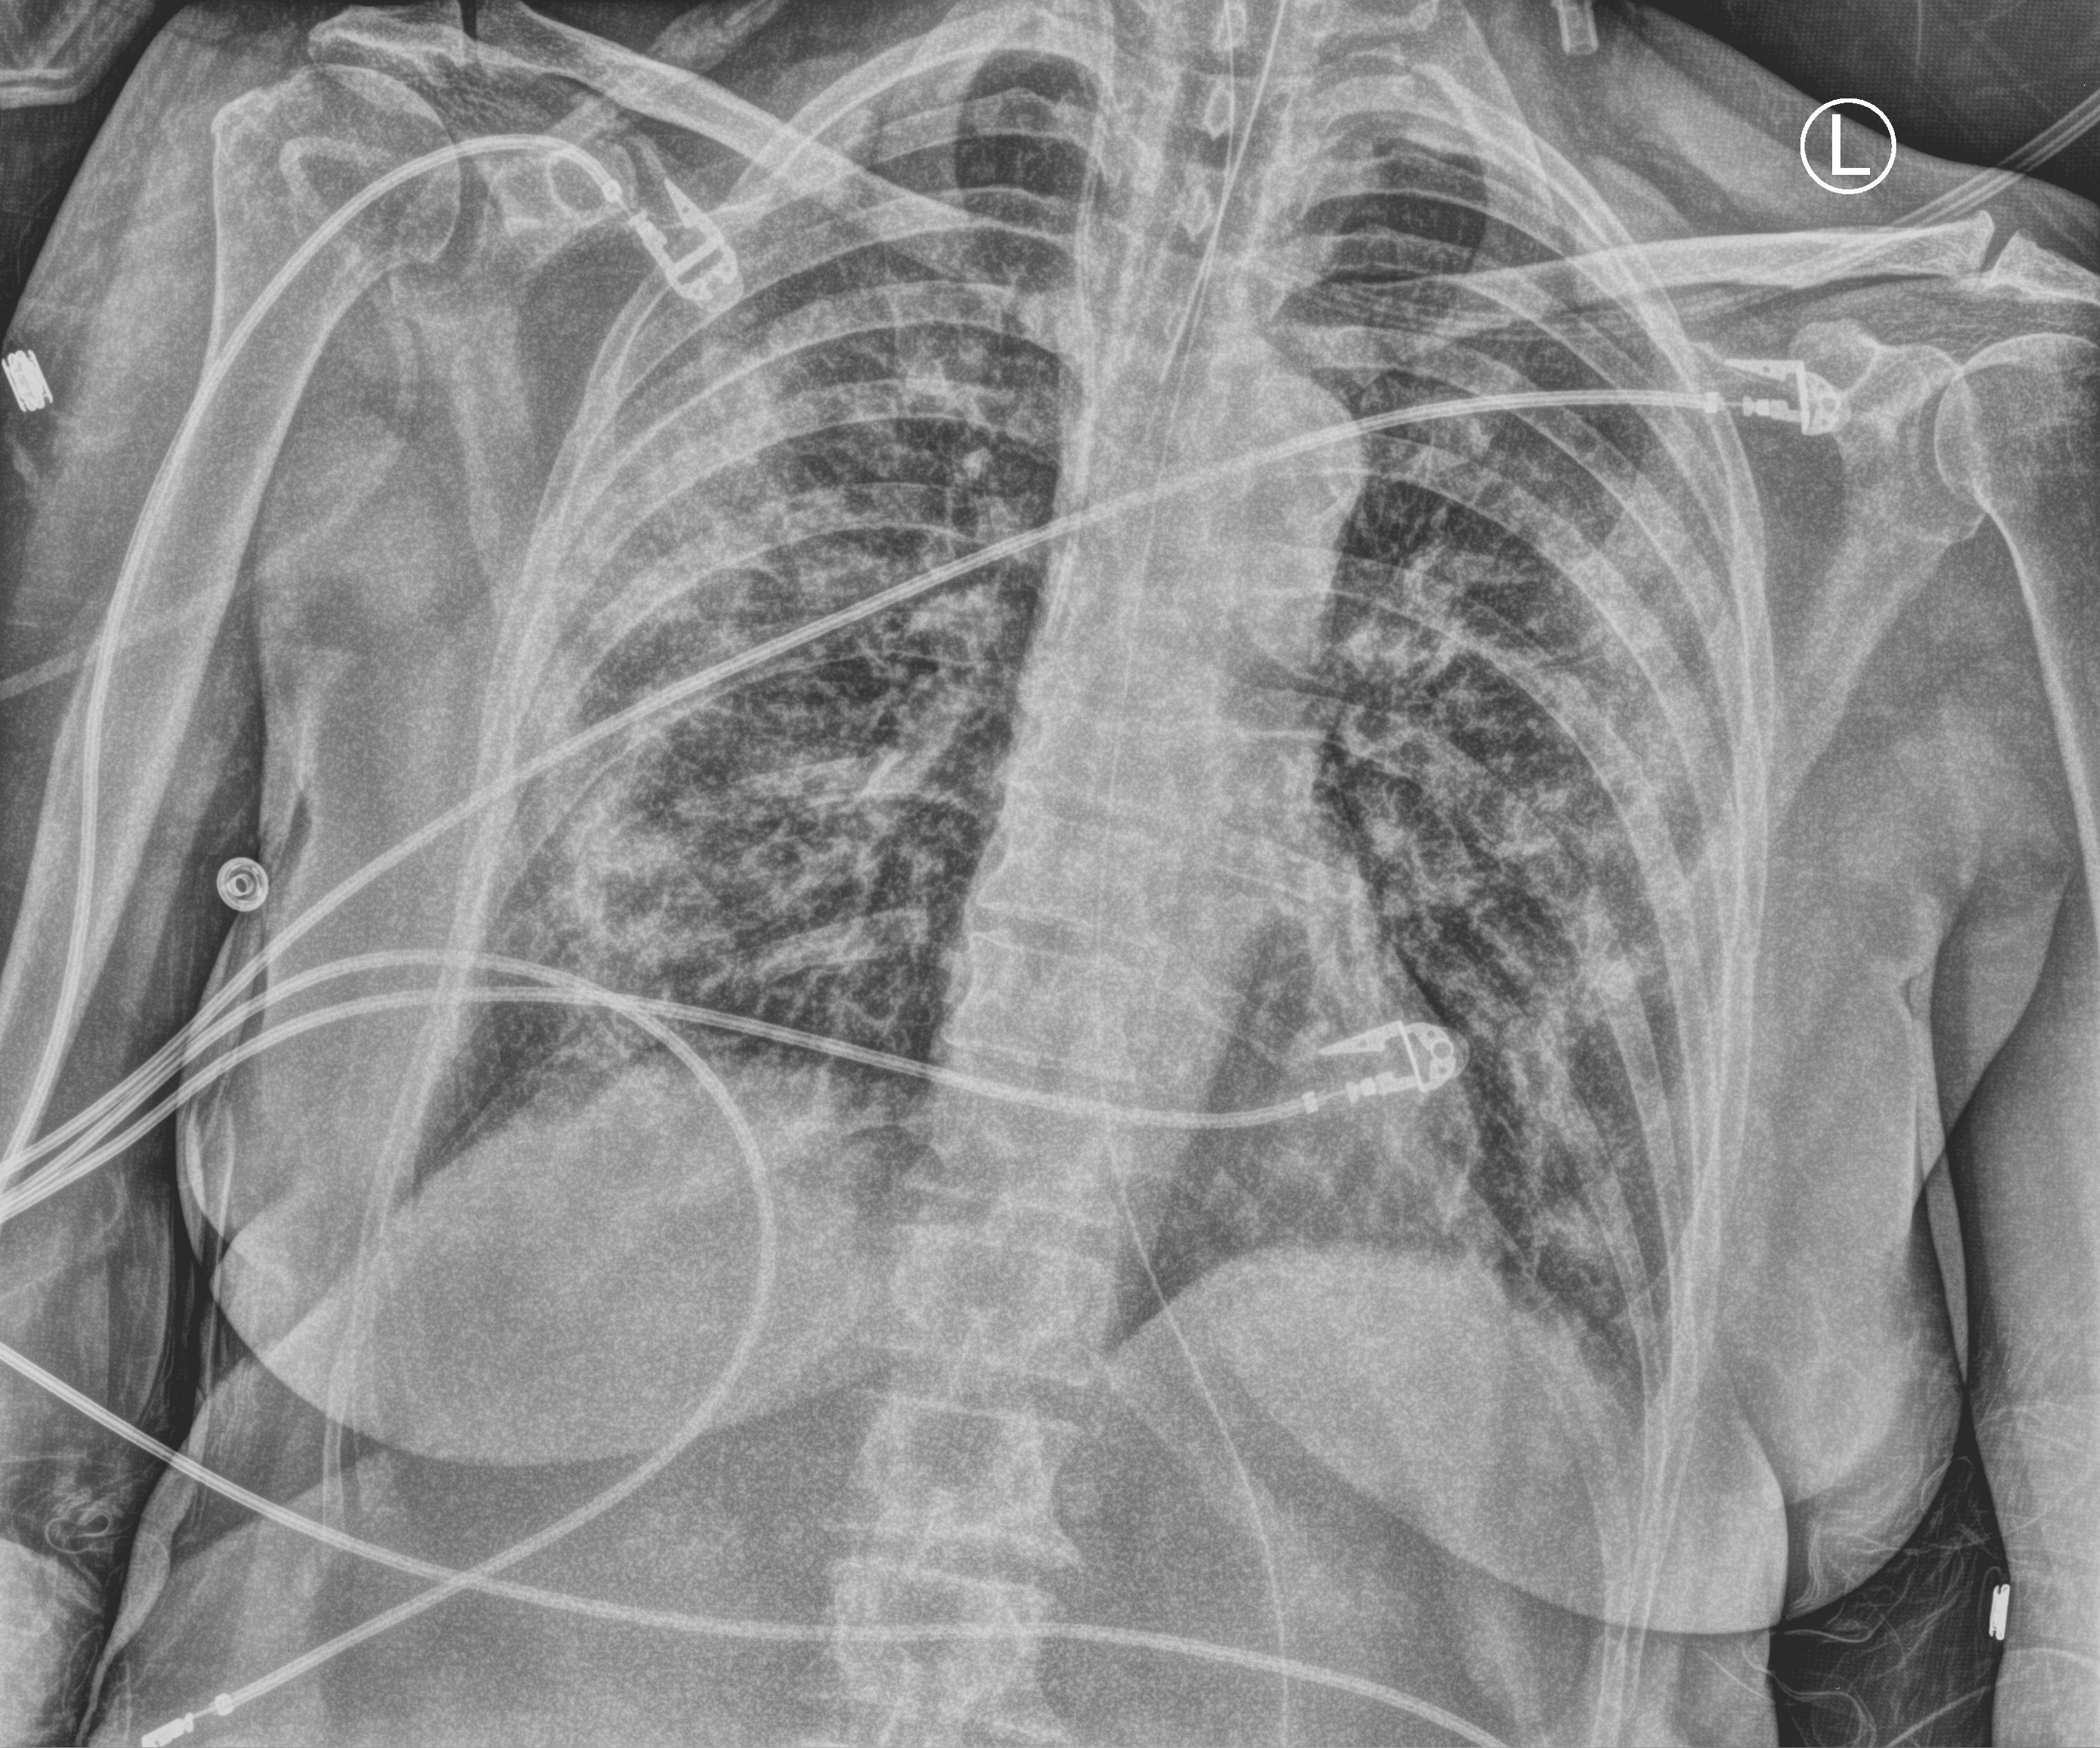
Portable chest radiograph, anteroposterior (AP) projection. Patient hospitalised with COVID-19; female, aged 60–74 years.
Hospital-stay facts (about this admission, not read from this image; timing relative to this image not recorded):
- mechanically ventilated during this hospital stay: yes
- length of hospital stay: 18 days